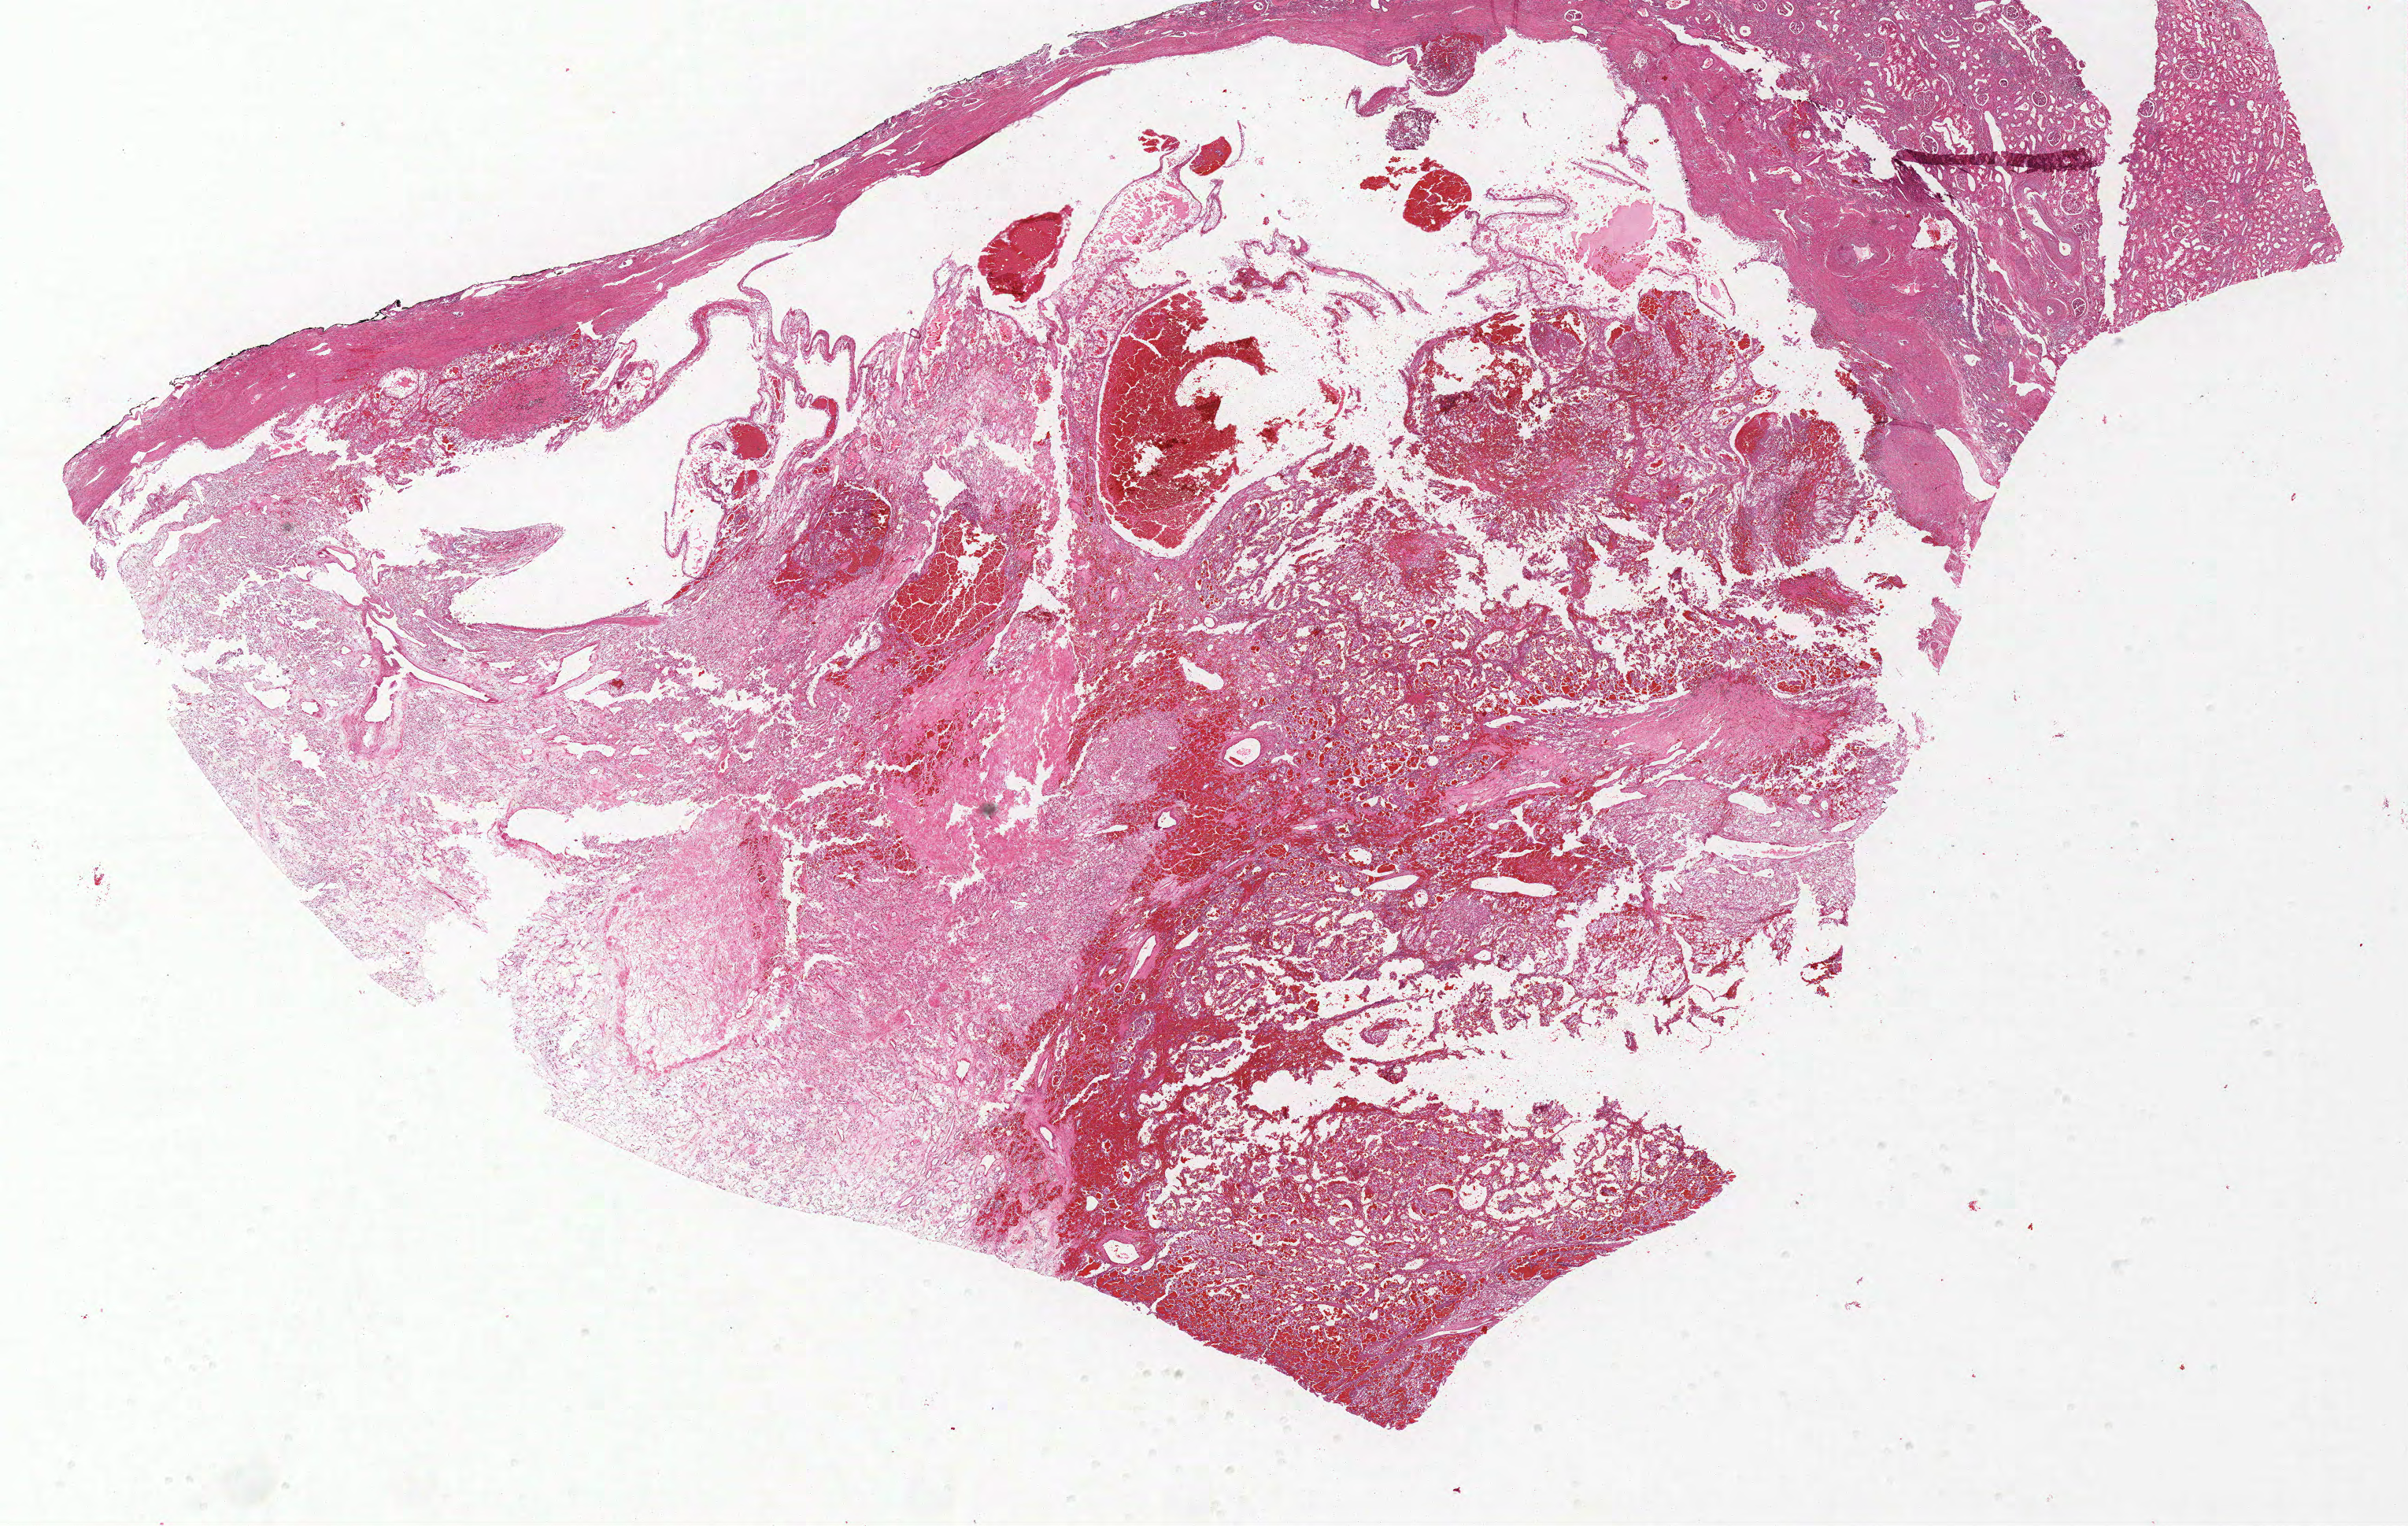
Whole-slide histology image, Hematoxylin and eosin (H&E) stained — low-resolution overview of the scanned area, about 24.5 x 15.5 mm, formalin-fixed paraffin-embedded (FFPE) diagnostic section, primary tumour sample from the kidney. Female, age 55 years at initial diagnosis. Histologic grade: G2 (moderately differentiated).
Pathologic diagnosis: Clear cell adenocarcinoma, NOS. AJCC pathologic stage: I.